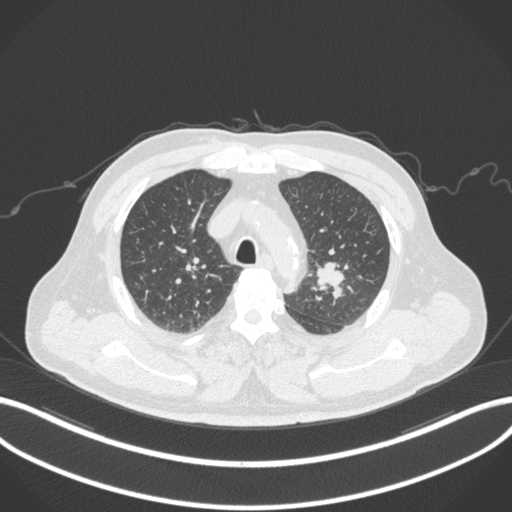
Chest CT, one axial slice; slice 231 of 286 in the series (ordered by position); reconstruction kernel B31f; 120 kVp; lung window (W 1500 / L -600 HU); 1 mm slice thickness; 512 × 512 image matrix, field of view 400 × 400 mm. Male patient, age 67 years. From the clinical record (not read from this slice): clinical TNM (as recorded): T2a N1 M0; histopathological grade: G3.
Outlined on this slice (bounding box drawn by a radiologist):
- lung tumour (recorded histology: adenocarcinoma): bounding box [x1, y1, x2, y2] px = [310, 257, 349, 301]